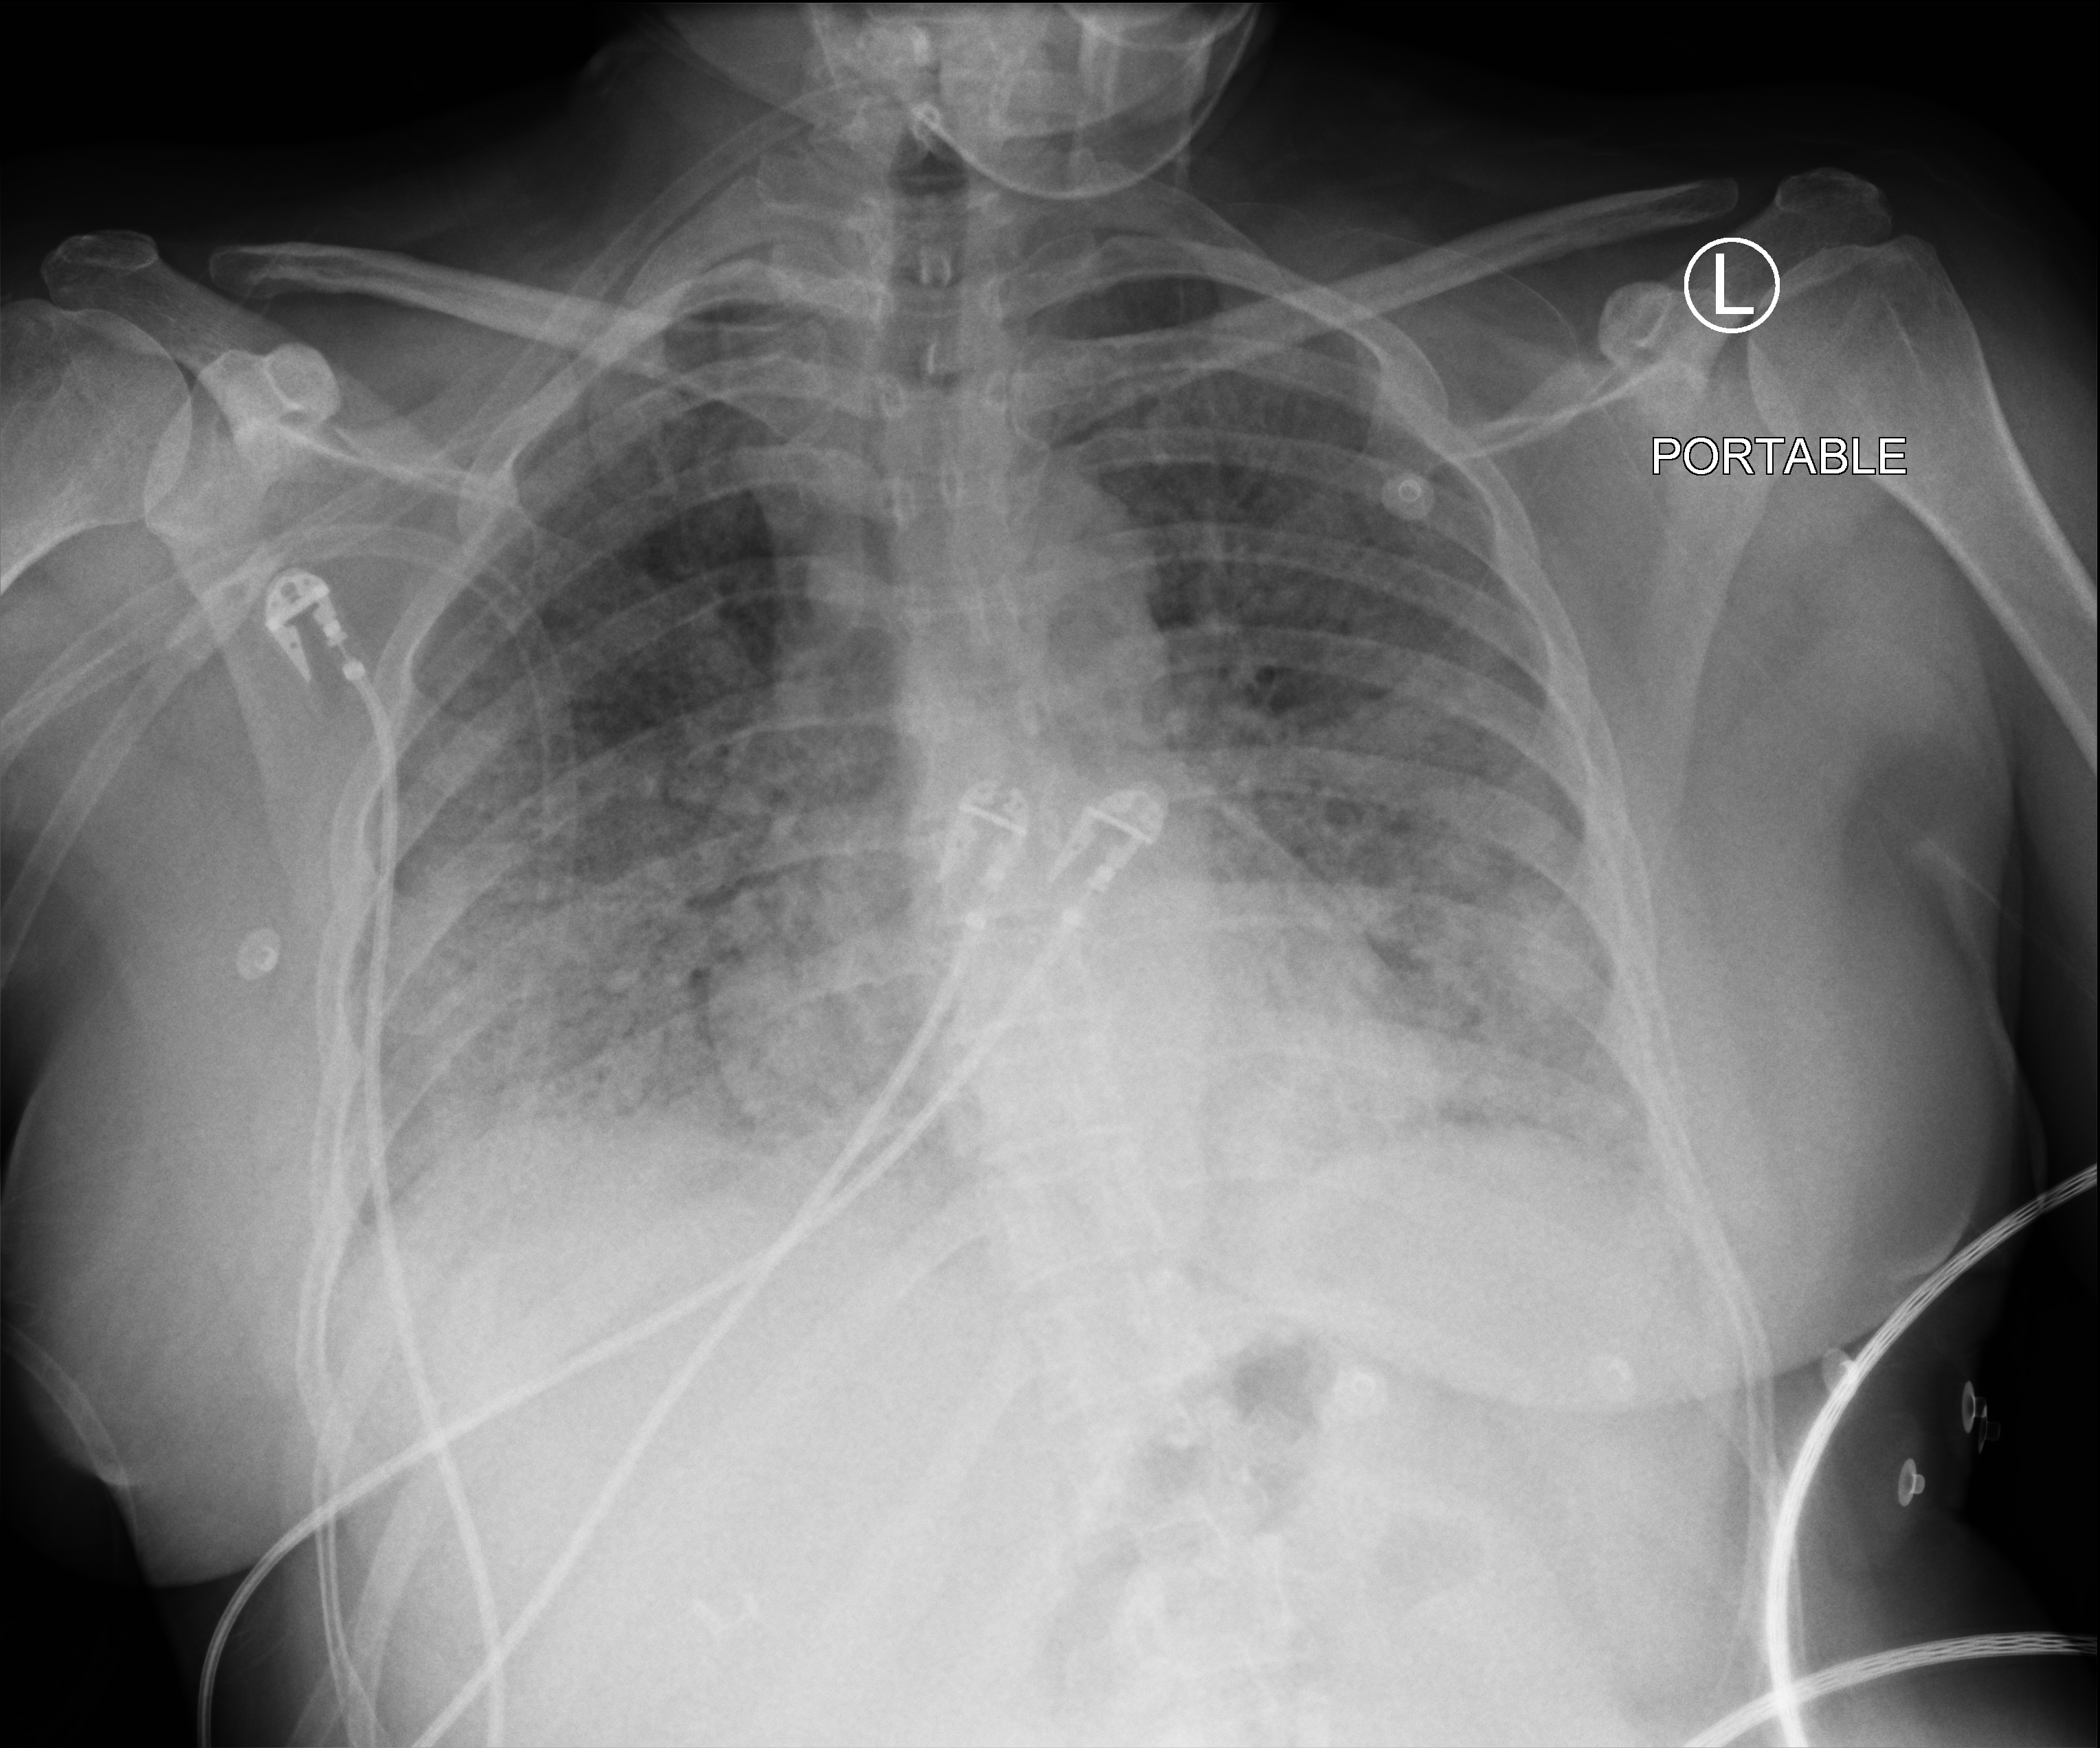
Portable chest radiograph, anteroposterior (AP) projection. Patient hospitalised with COVID-19; female, aged 18–59 years.
Hospital-stay facts (about this admission, not read from this image; timing relative to this image not recorded): other chronic lung disease (admission record): no; mechanically ventilated during this hospital stay: no; admitted to intensive care during this hospital stay: no.